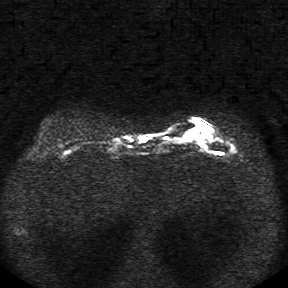
Breast MRI, one axial slice. Position 8 of 34 along the scan axis. Diffusion-weighted series; image 2 of 4 stored at this slice position (different b-values; order by instance number). 1.5 T. 5 mm slice thickness. 288 × 288 image matrix. Female patient.
Annotated regions visible in this slice (outlined manually by an expert reader):
- tumour on diffusion-weighted imaging: bounding box [x1, y1, x2, y2] px = [185, 121, 212, 140]